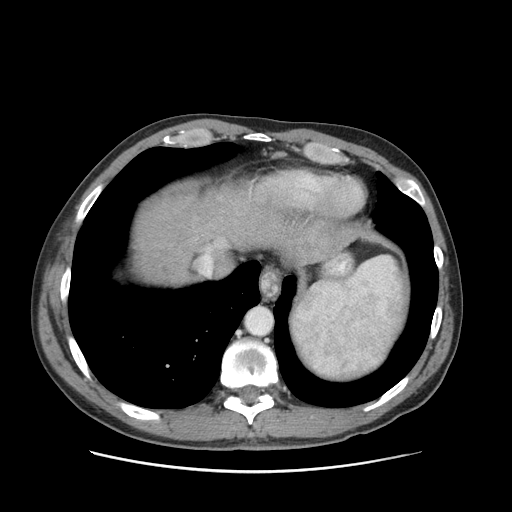
Contrast-enhanced abdominal CT (liver protocol), one axial slice. Slice 83 of 93 in the series (ordered by position). Soft-tissue window (W 400 / L 40 HU). 2.5 mm slice thickness. 512 × 512 image matrix, field of view 380 × 380 mm. From the clinical record (not read from this slice): diagnosis: hepatocellular carcinoma (patient treated with transarterial chemoembolisation; whether this scan precedes or follows treatment is not stated here); TNM stage (as recorded): Stage-II; Child-Pugh class: A; tumour differentiation: moderately differentiated.
Annotated regions visible in this slice (semi-automatic segmentation, software-assisted and operator-edited):
- abdominal aorta: bounding box <245,308,272,335> (left, top, right, bottom; pixels)
- liver parenchyma outside the tumour (the mass and vessels are separate outlines, so this box may not span the whole liver): <132,186,344,284>